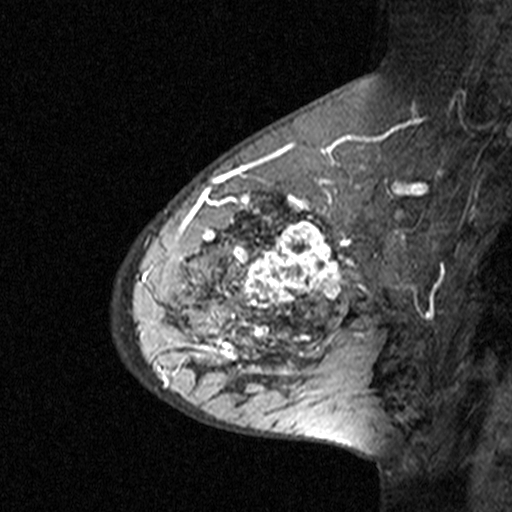
Breast MRI (dynamic contrast-enhanced), one sagittal slice. Position 26 of 44 along the scan axis. Dynamic contrast-enhanced study with each time point stored as its own series, time point 3 of 4 at this slice position (ordered by acquisition time). 1.5 T. TE 4.5 ms, TR 11 ms. 3 mm slice thickness. 512 × 512 image matrix, field of view 200 × 200 mm. Patient: female, 65 years. Case-level facts recorded for this patient, not image findings: setting: breast cancer imaged before/during neoadjuvant chemotherapy; receptor status: HER2-positive.
Structures marked on this image (semi-automatic segmentation, software-assisted and operator-edited):
- analysis volume of interest (the breast-tissue region the enhancement analysis was run in; not a lesion): box from (x=182, y=190) to (x=353, y=361) px
- tumour enhancement mask (voxels above the 90 % enhancement threshold inside the analysis volume of interest): (x=182, y=190)–(x=353, y=359)